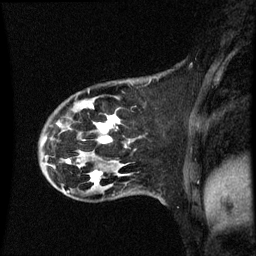
Breast MRI (dynamic contrast-enhanced), one sagittal slice. Position 16 of 60 along the scan axis. Dynamic contrast-enhanced series, image 2 of 3 at this slice position (ordered by acquisition). 1.5 T. TE 4.2 ms, TR 8.9 ms. 2 mm slice thickness. 256 × 256 image matrix, field of view 200 × 200 mm. Patient: female, 44 years. Case-level facts recorded for this patient, not image findings: setting: breast cancer imaged before/during neoadjuvant chemotherapy; receptor status: HR-positive, HER2-negative.
Structures marked on this image (semi-automatic segmentation, software-assisted and operator-edited):
- analysis volume of interest (the breast-tissue region the enhancement analysis was run in; not a lesion): bounding box (x1, y1, x2, y2) in pixels: (43, 80, 151, 189)
- tumour enhancement mask (voxels above the 70 % enhancement threshold inside the analysis volume of interest): (66, 116, 120, 185)